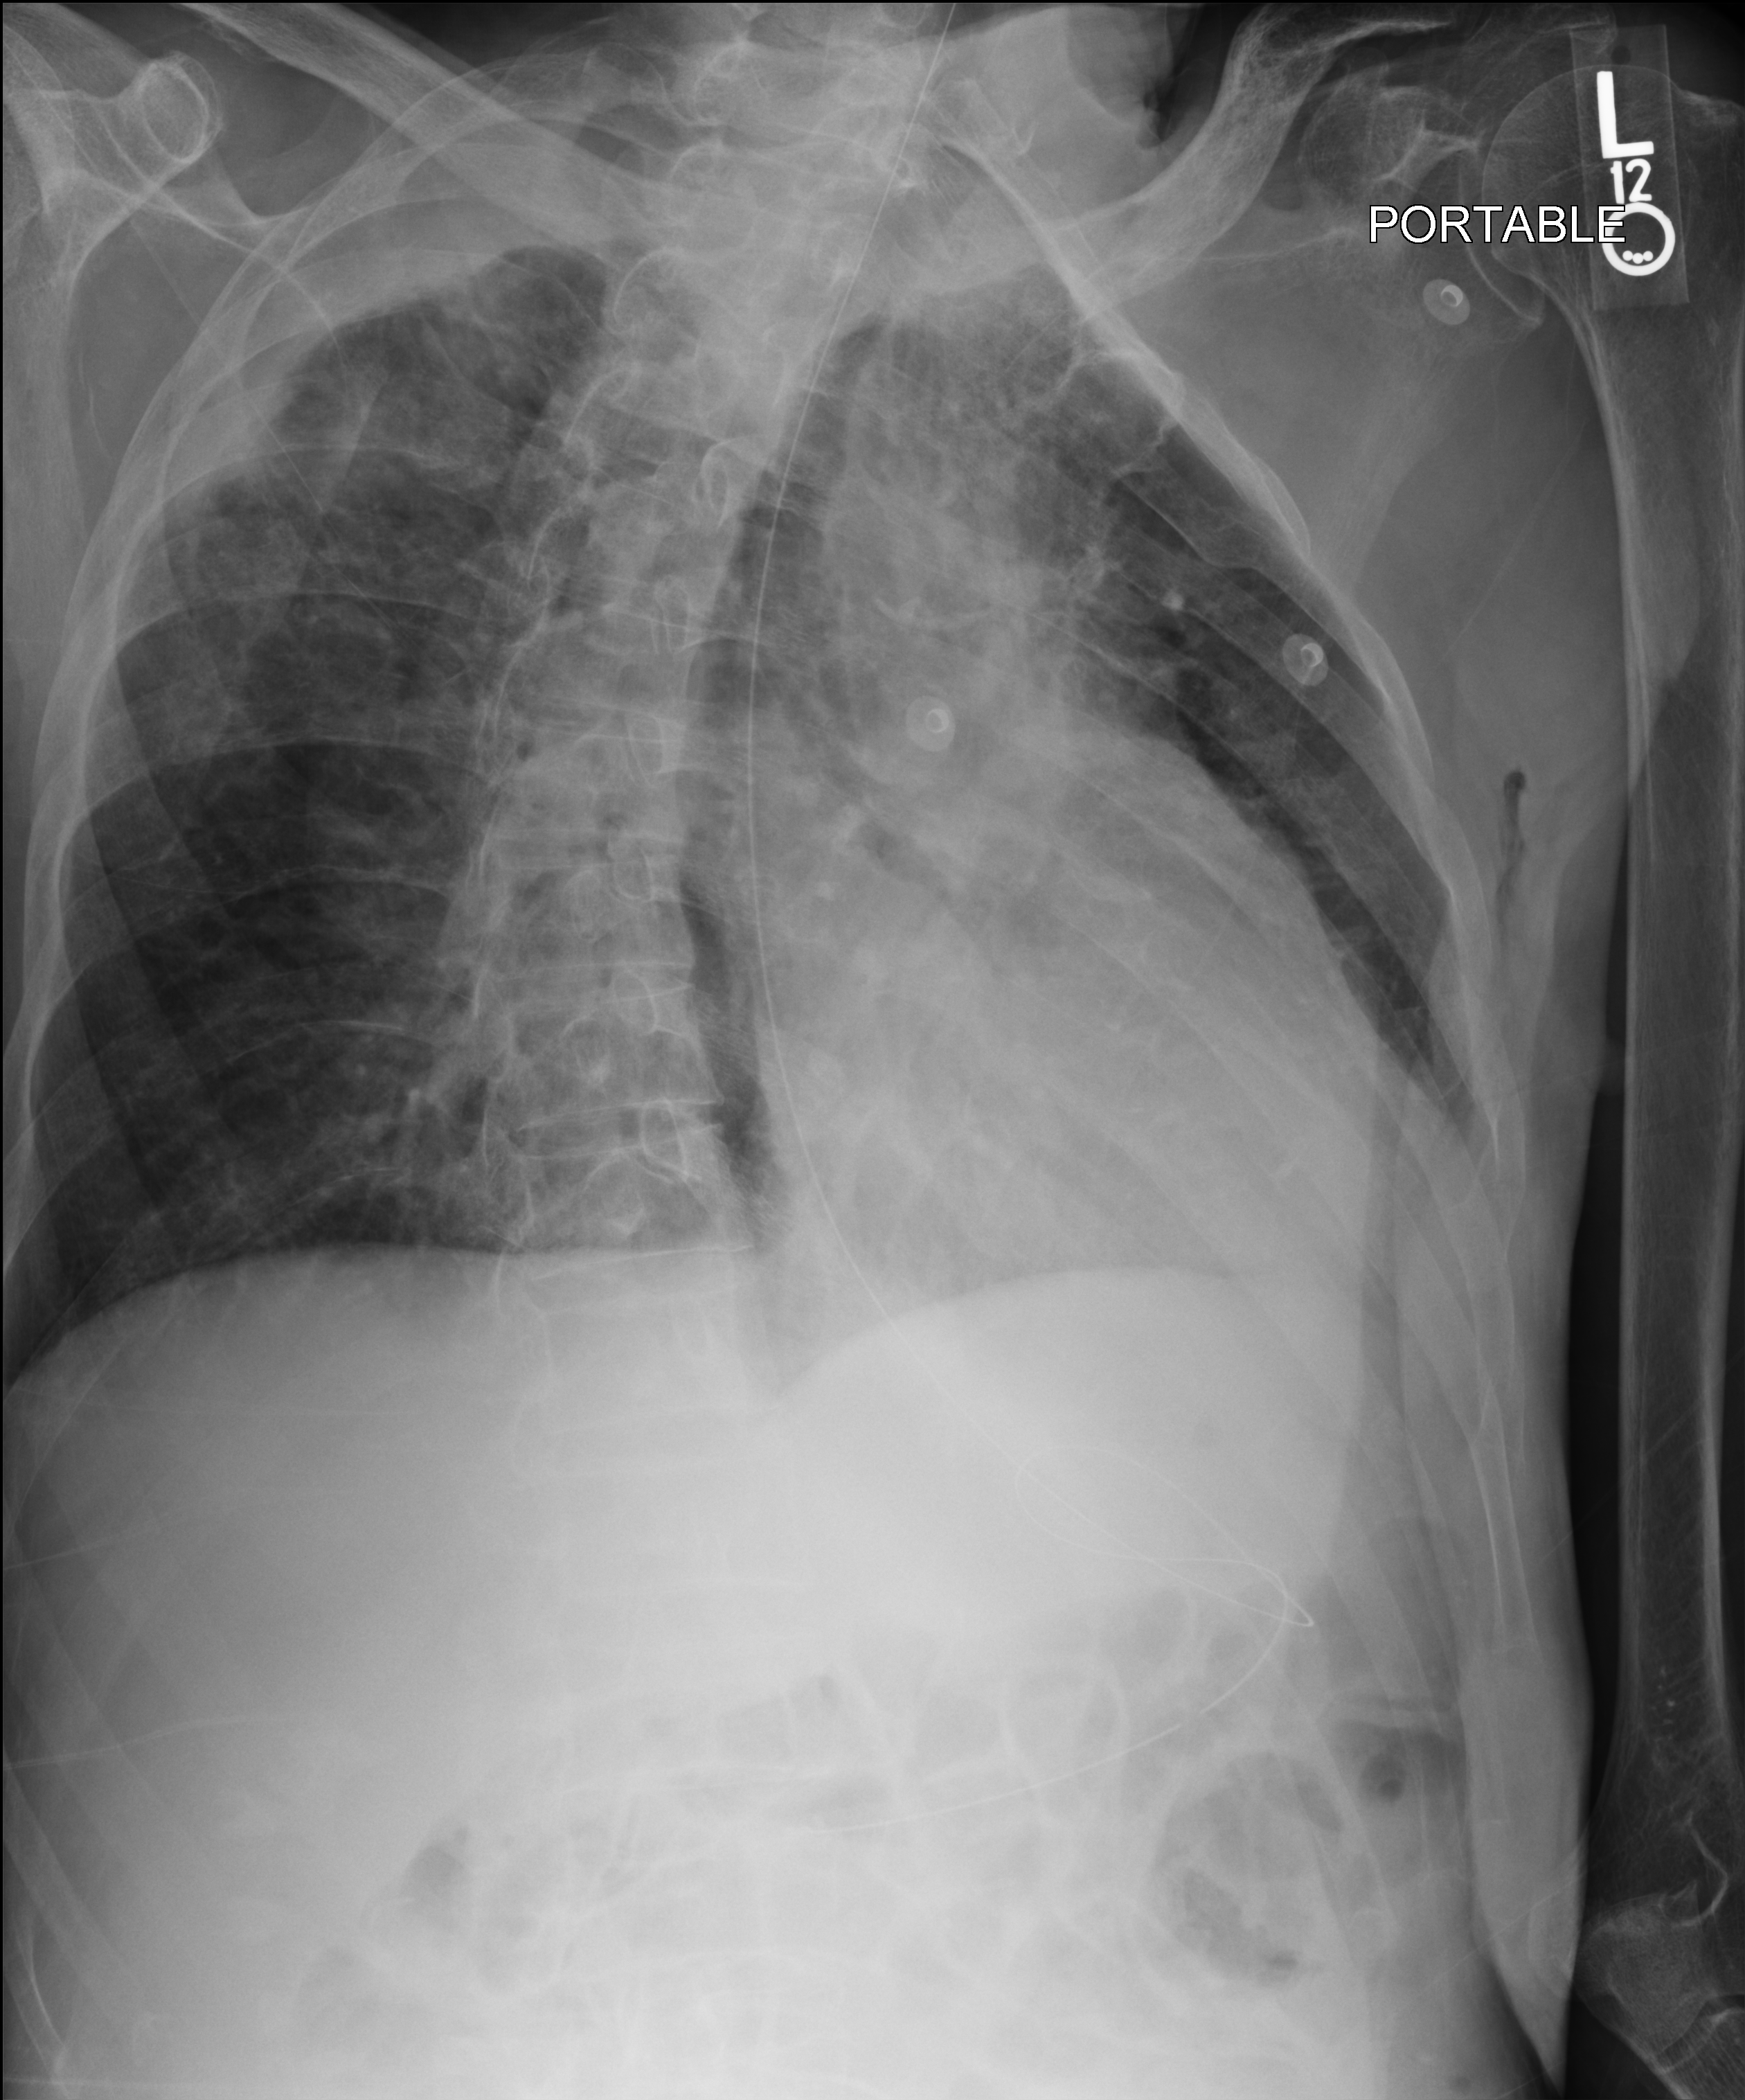
Bedside chest radiograph (computed radiography), anteroposterior (AP) projection. Male patient hospitalised with COVID-19, age 75–90 years.
Hospital-stay facts (about this admission, not read from this image; timing relative to this image not recorded):
- chronic kidney disease (admission record): no
- admitted to intensive care during this hospital stay: no
- hypertension (admission record): yes